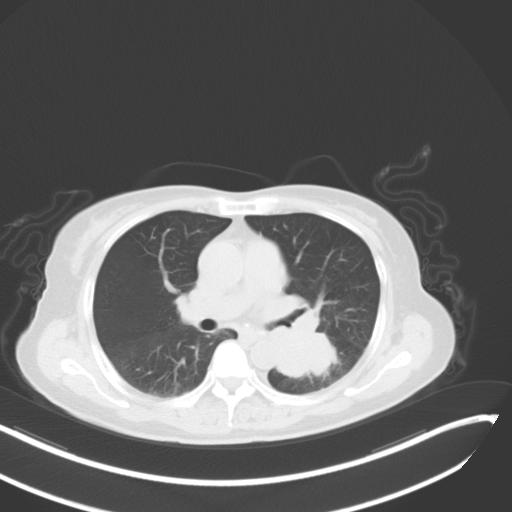
Chest CT, one axial slice. Slice 22 of 48 in the series (ordered by position). 120 kVp. Lung window (W 1500 / L -600 HU). 5 mm slice thickness. 512 × 512 image matrix. Patient: female, 64 years. From the clinical record (not read from this slice): clinical TNM (as recorded): T3 N1 M1; histopathological grade: G3.
Annotated regions visible in this slice (bounding box drawn by a radiologist):
- lung tumour (recorded histology: small cell carcinoma): bounding box [x1, y1, x2, y2] px = [263, 319, 343, 380]